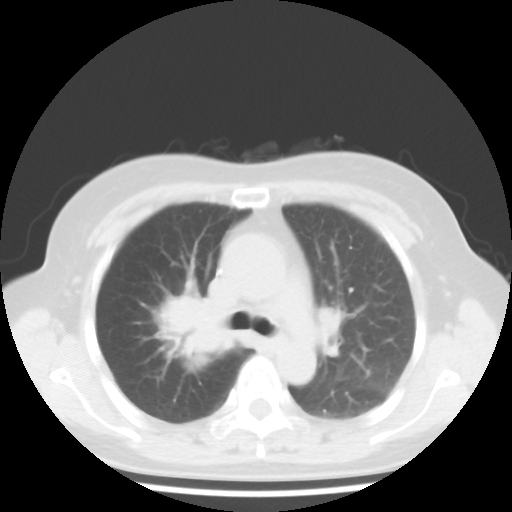
Chest CT, one axial slice; position 27 of 43 along the scan axis; reconstruction kernel STANDARD; 100 kVp; lung window (W 1500 / L -600 HU); 5 mm slice thickness; 512 × 512 image matrix, field of view 316 × 316 mm. Female patient, age 62 years. Case-level facts recorded for this patient, not image findings: clinical TNM (as recorded): T3 N0 M0; histopathological grade: G3.
Structures marked on this image (rectangle marked by the reading radiologist):
- lung tumour (recorded histology: small cell carcinoma): bounding box (x1, y1, x2, y2) in pixels: (154, 278, 246, 366)